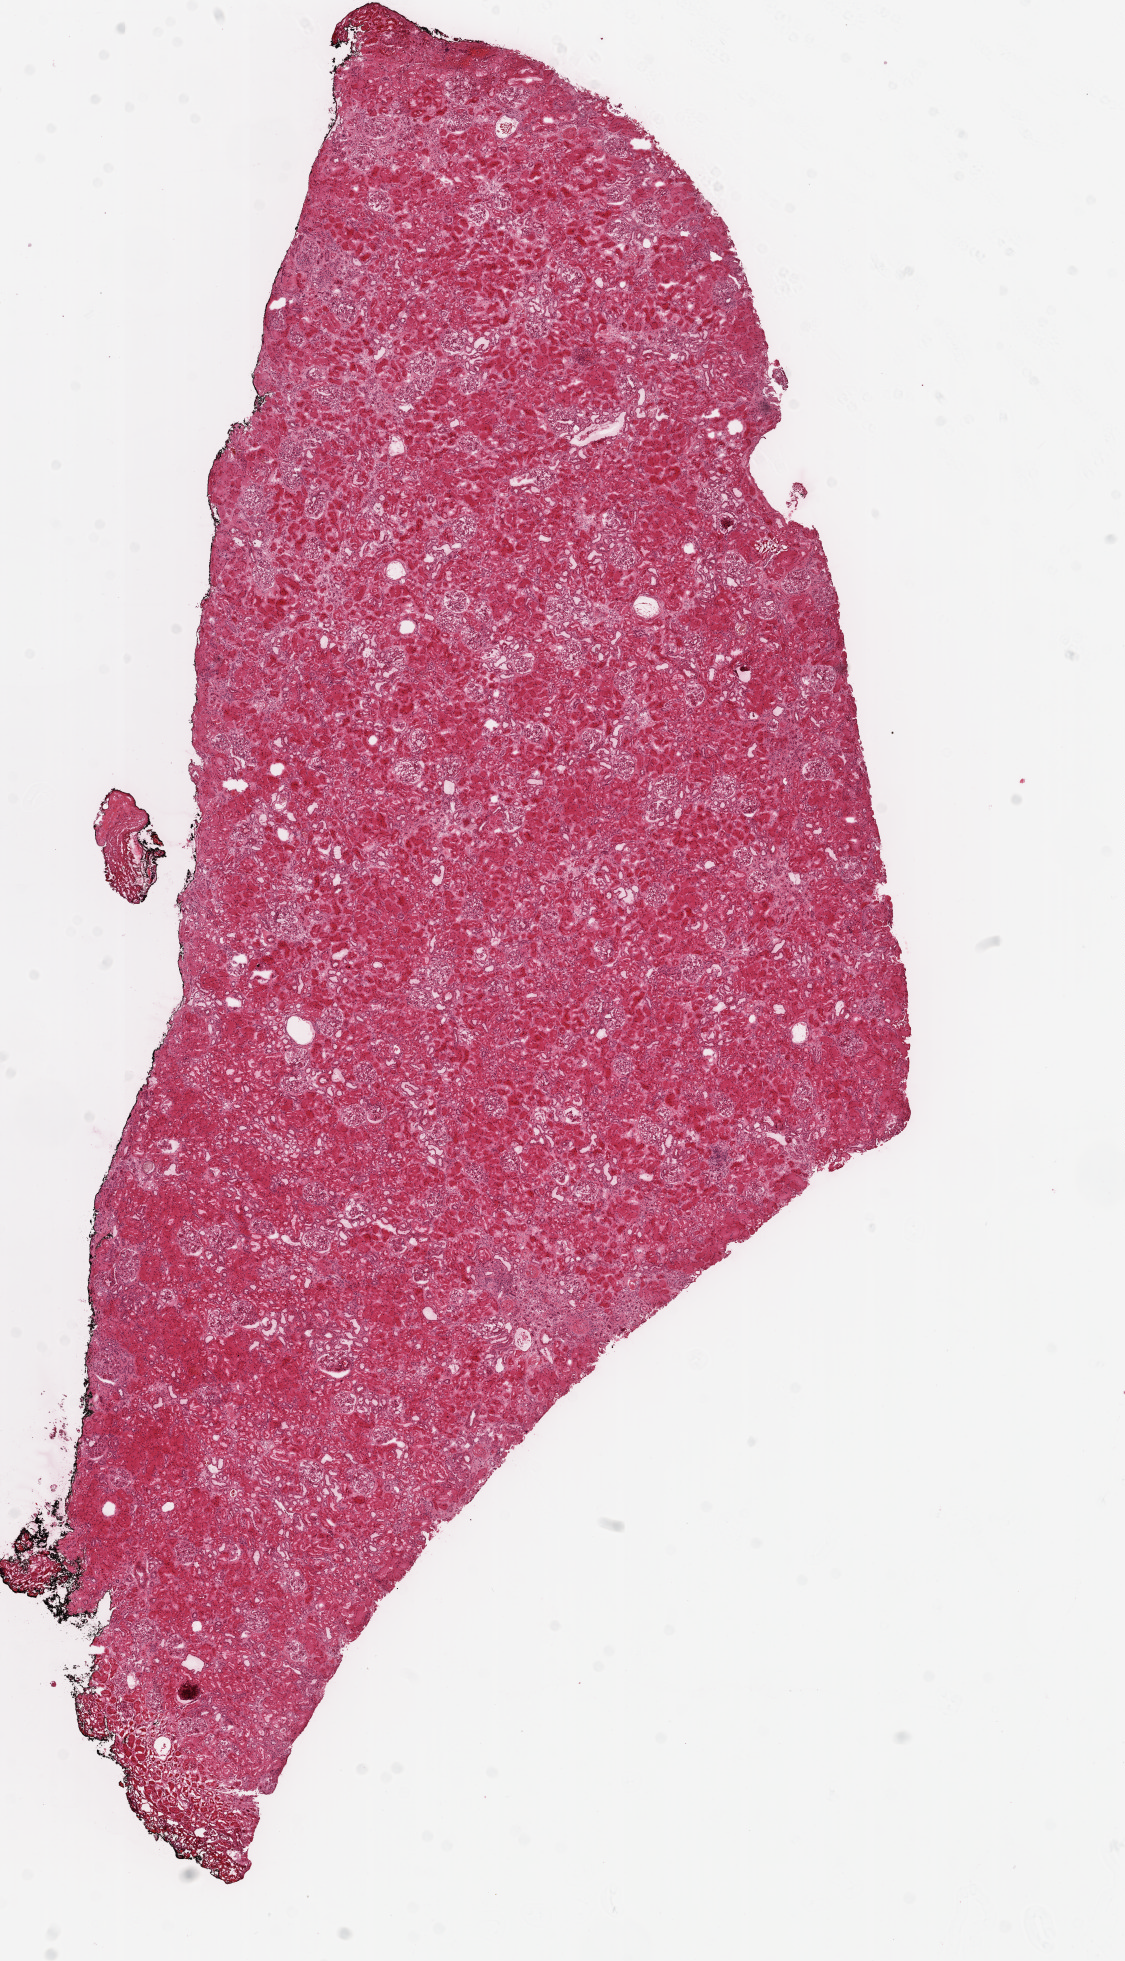
H&E-stained whole-slide image — a low-resolution overview of the entire scanned area, about 9.0 x 15.7 mm, frozen section from the top of the tissue portion, kidney, solid tissue normal (non-tumour tissue) sample. Male patient; age at initial diagnosis 61 years.
- this section: solid tissue normal (non-tumour) sample from the same patient
- patient diagnosis: Clear cell adenocarcinoma, NOS